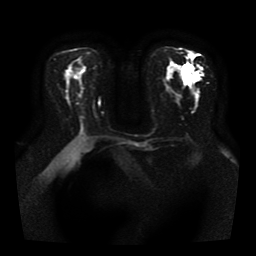
Breast MRI, one axial slice. Position 20 of 41 along the scan axis. Diffusion-weighted series; image 2 of 4 stored at this slice position (different b-values; order by instance number). 1.5 T. 5 mm slice thickness. 256 × 256 image matrix, field of view 330 × 330 mm. Female patient.
Structures marked on this image (outlined manually by an expert reader):
- tumour on diffusion-weighted imaging: bounding box <185,67,199,82> (left, top, right, bottom; pixels)